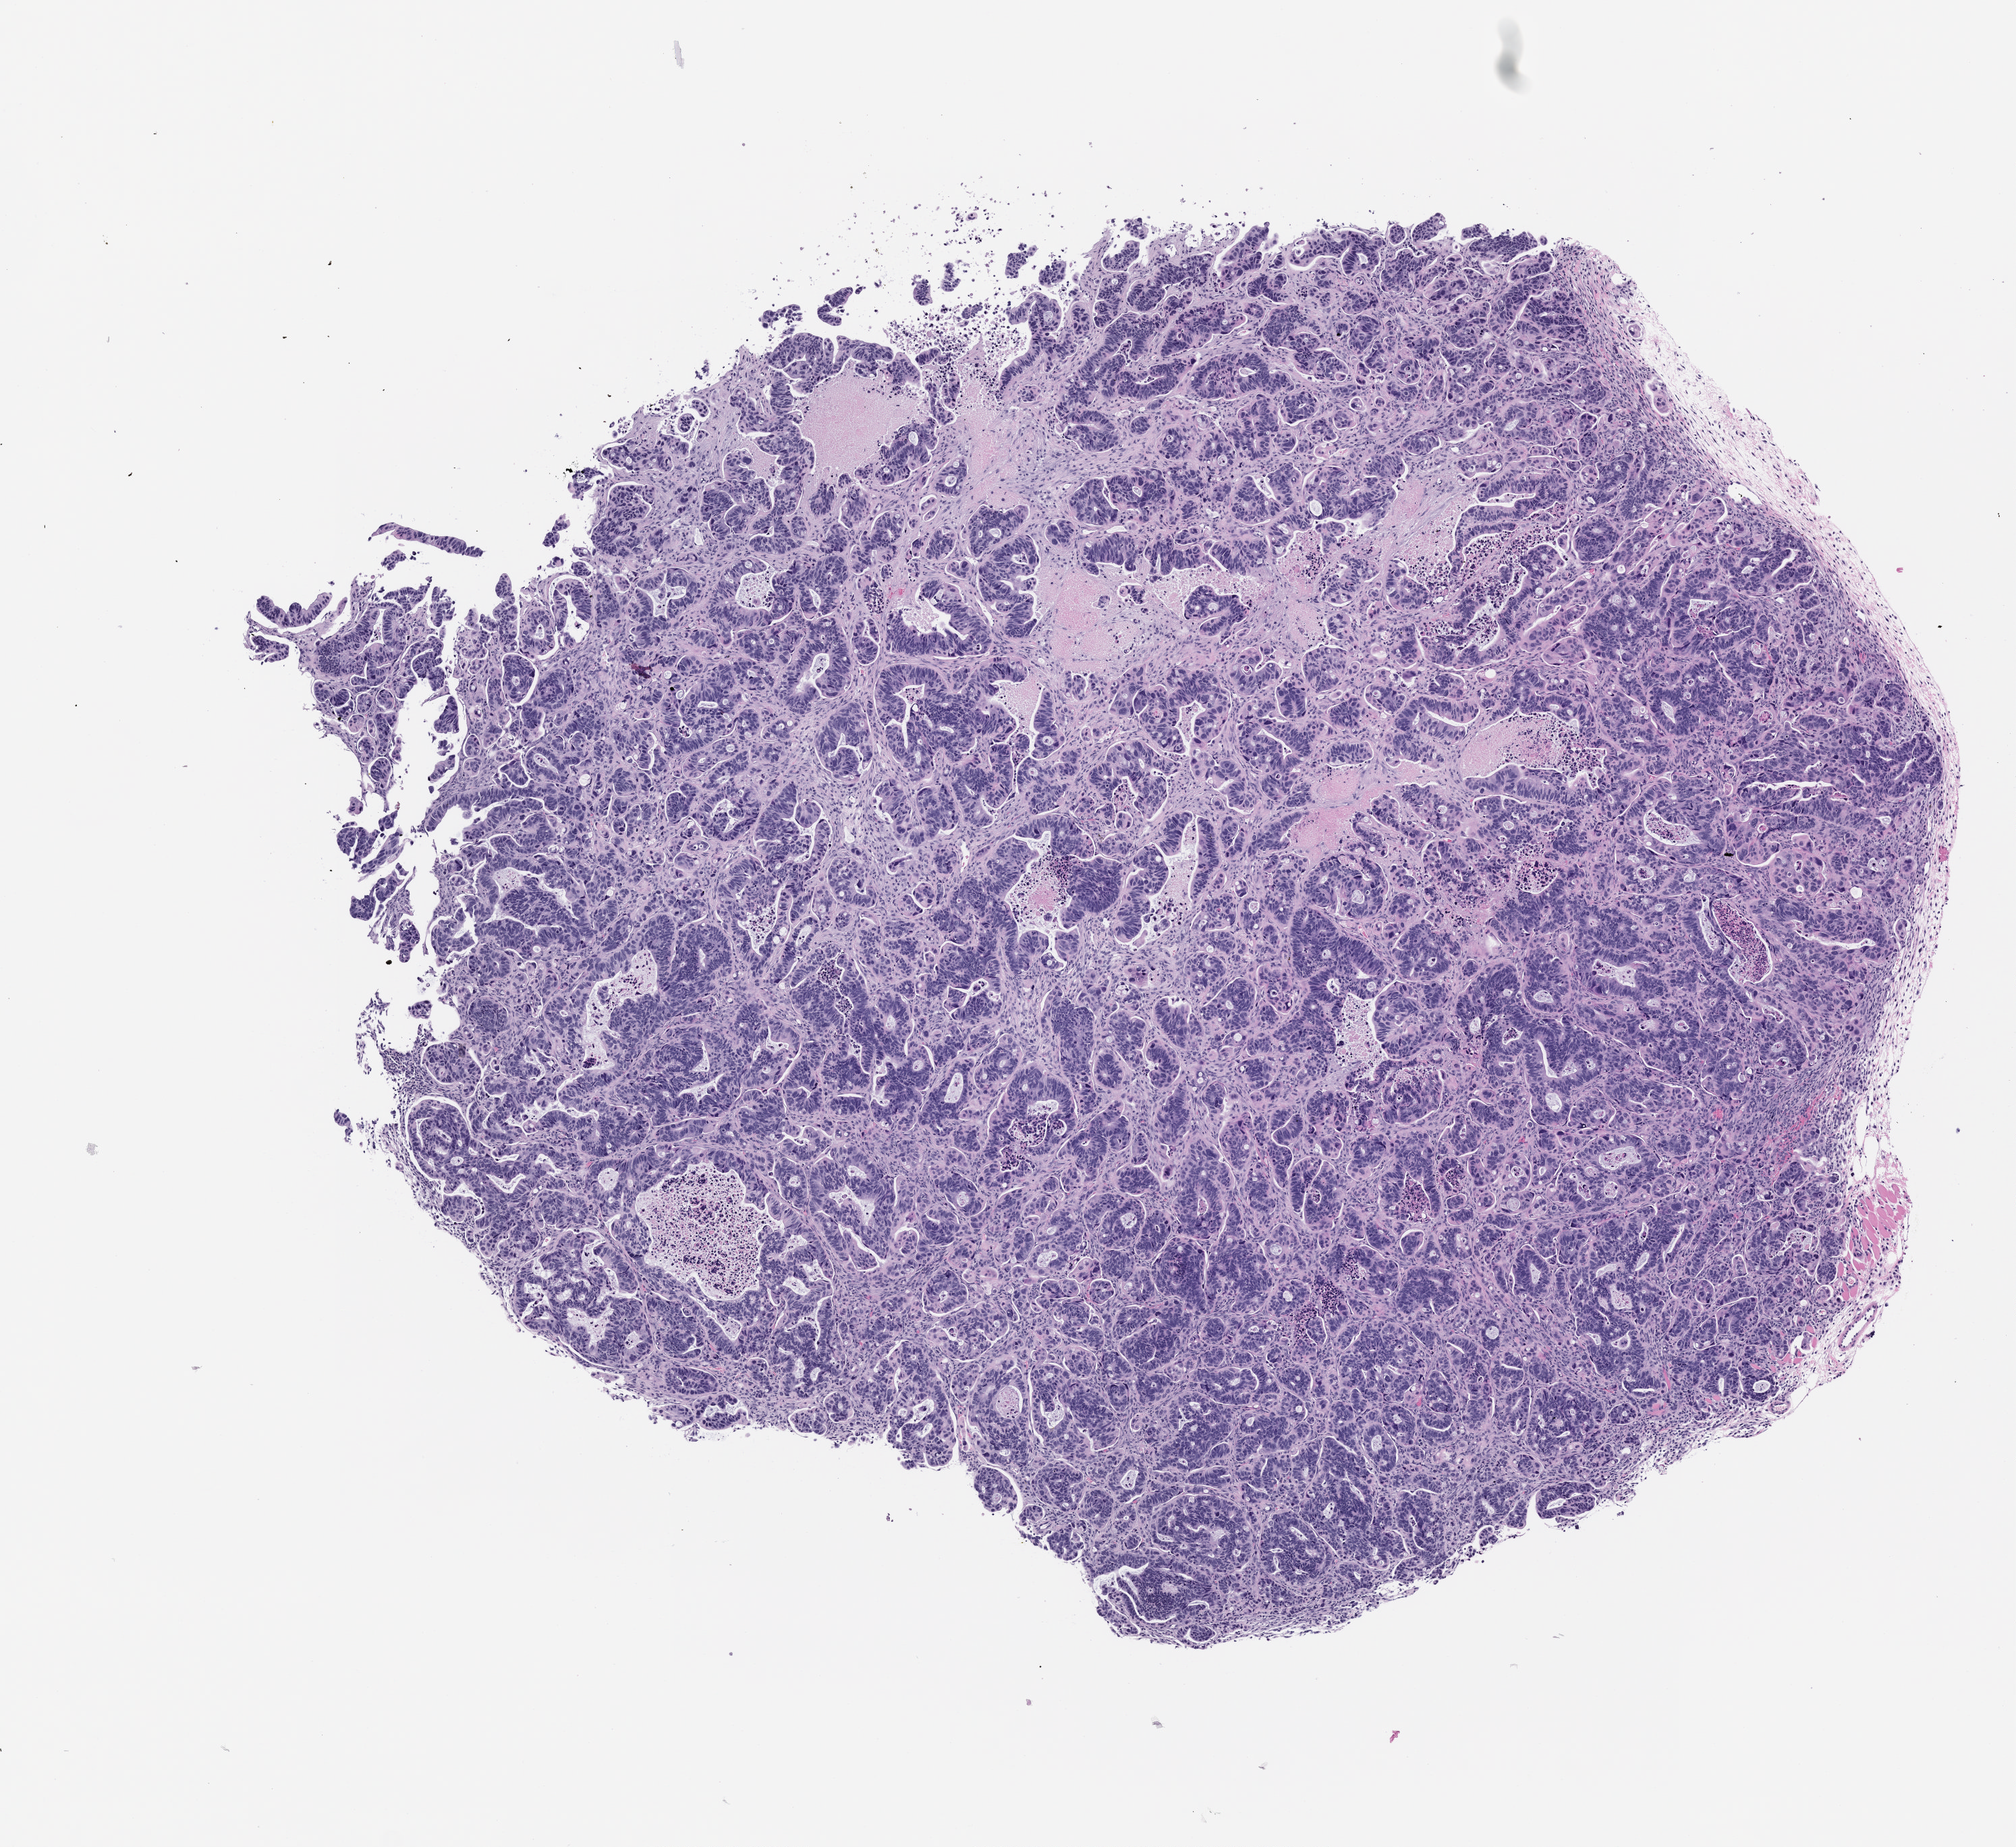
Whole-slide image, hematoxylin and eosin (H&E): patient-derived xenograft (human tumor grown in a mouse), passage 2 — shown as a low-resolution overview of the whole scanned area (about 6.0 x 5.5 mm); formalin-fixed, paraffin-embedded (FFPE) tissue; originating tumor site category: colon.
Originating patient diagnosis: Colon Adenocarcinoma.